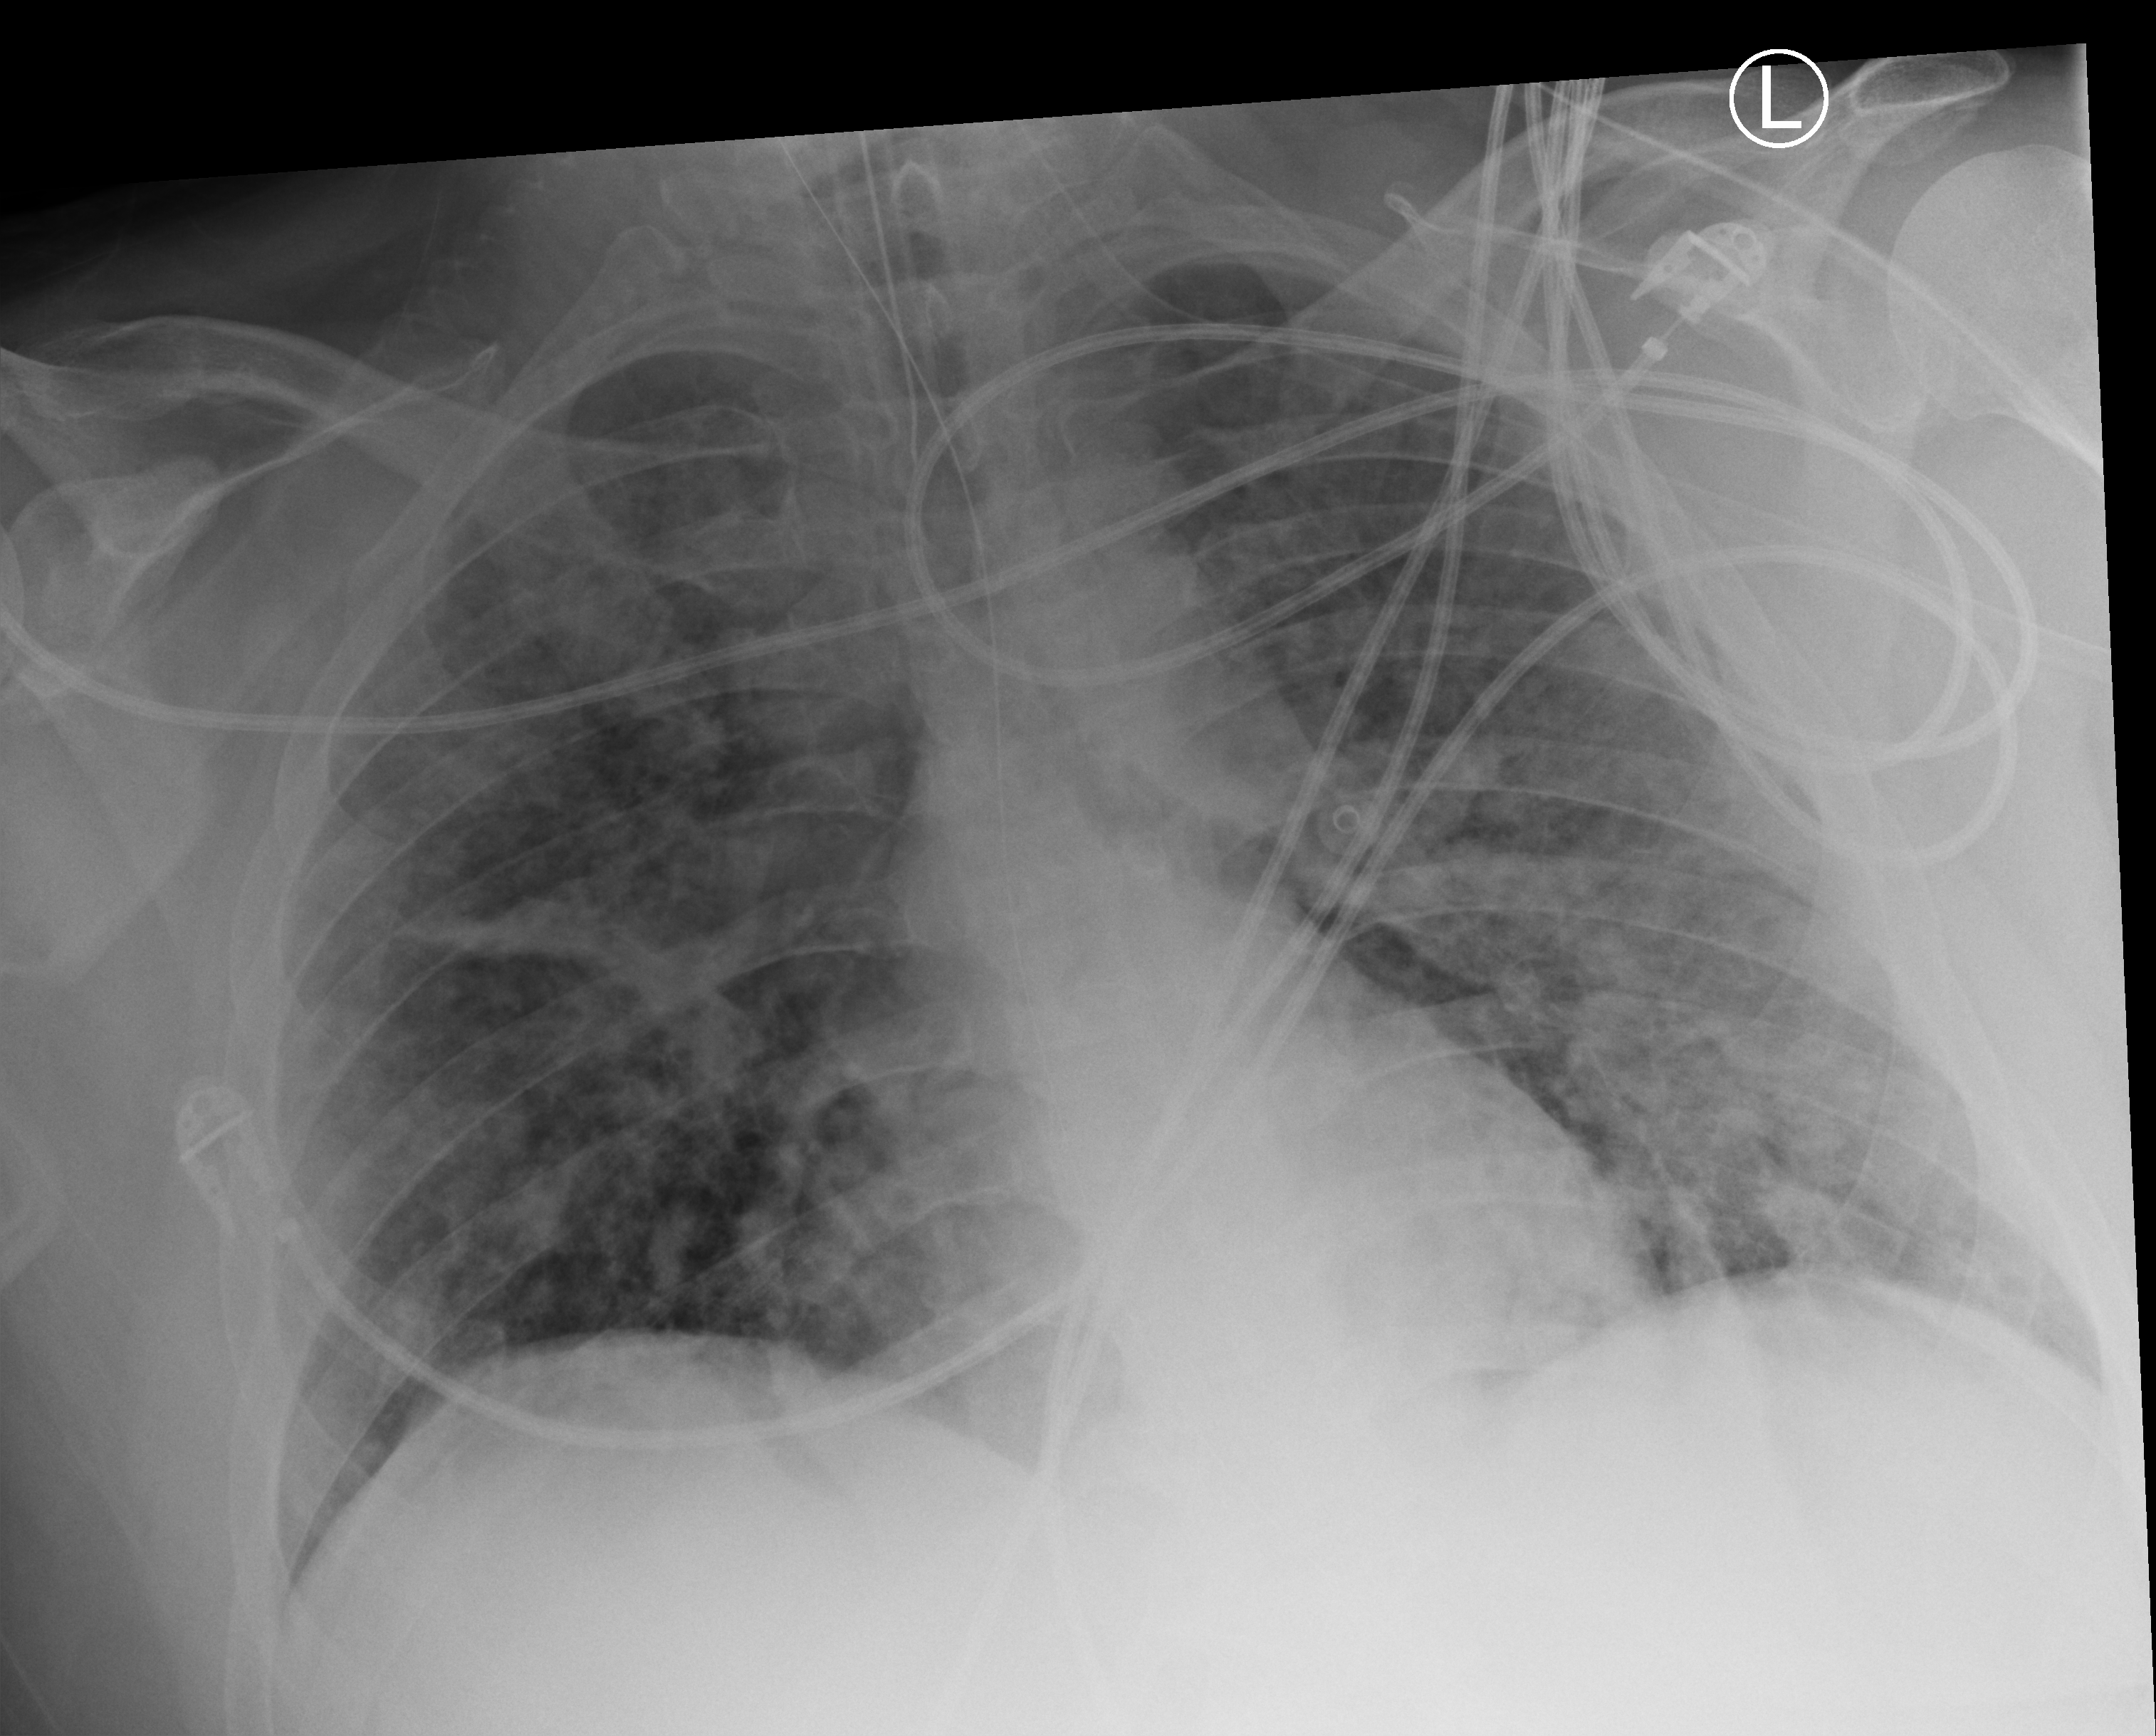
Portable chest radiograph. Patient hospitalised with COVID-19, aged 18–59 years.
Admission-level facts for this patient (not findings on this image; timing relative to this image not recorded): mechanically ventilated during this hospital stay: yes.